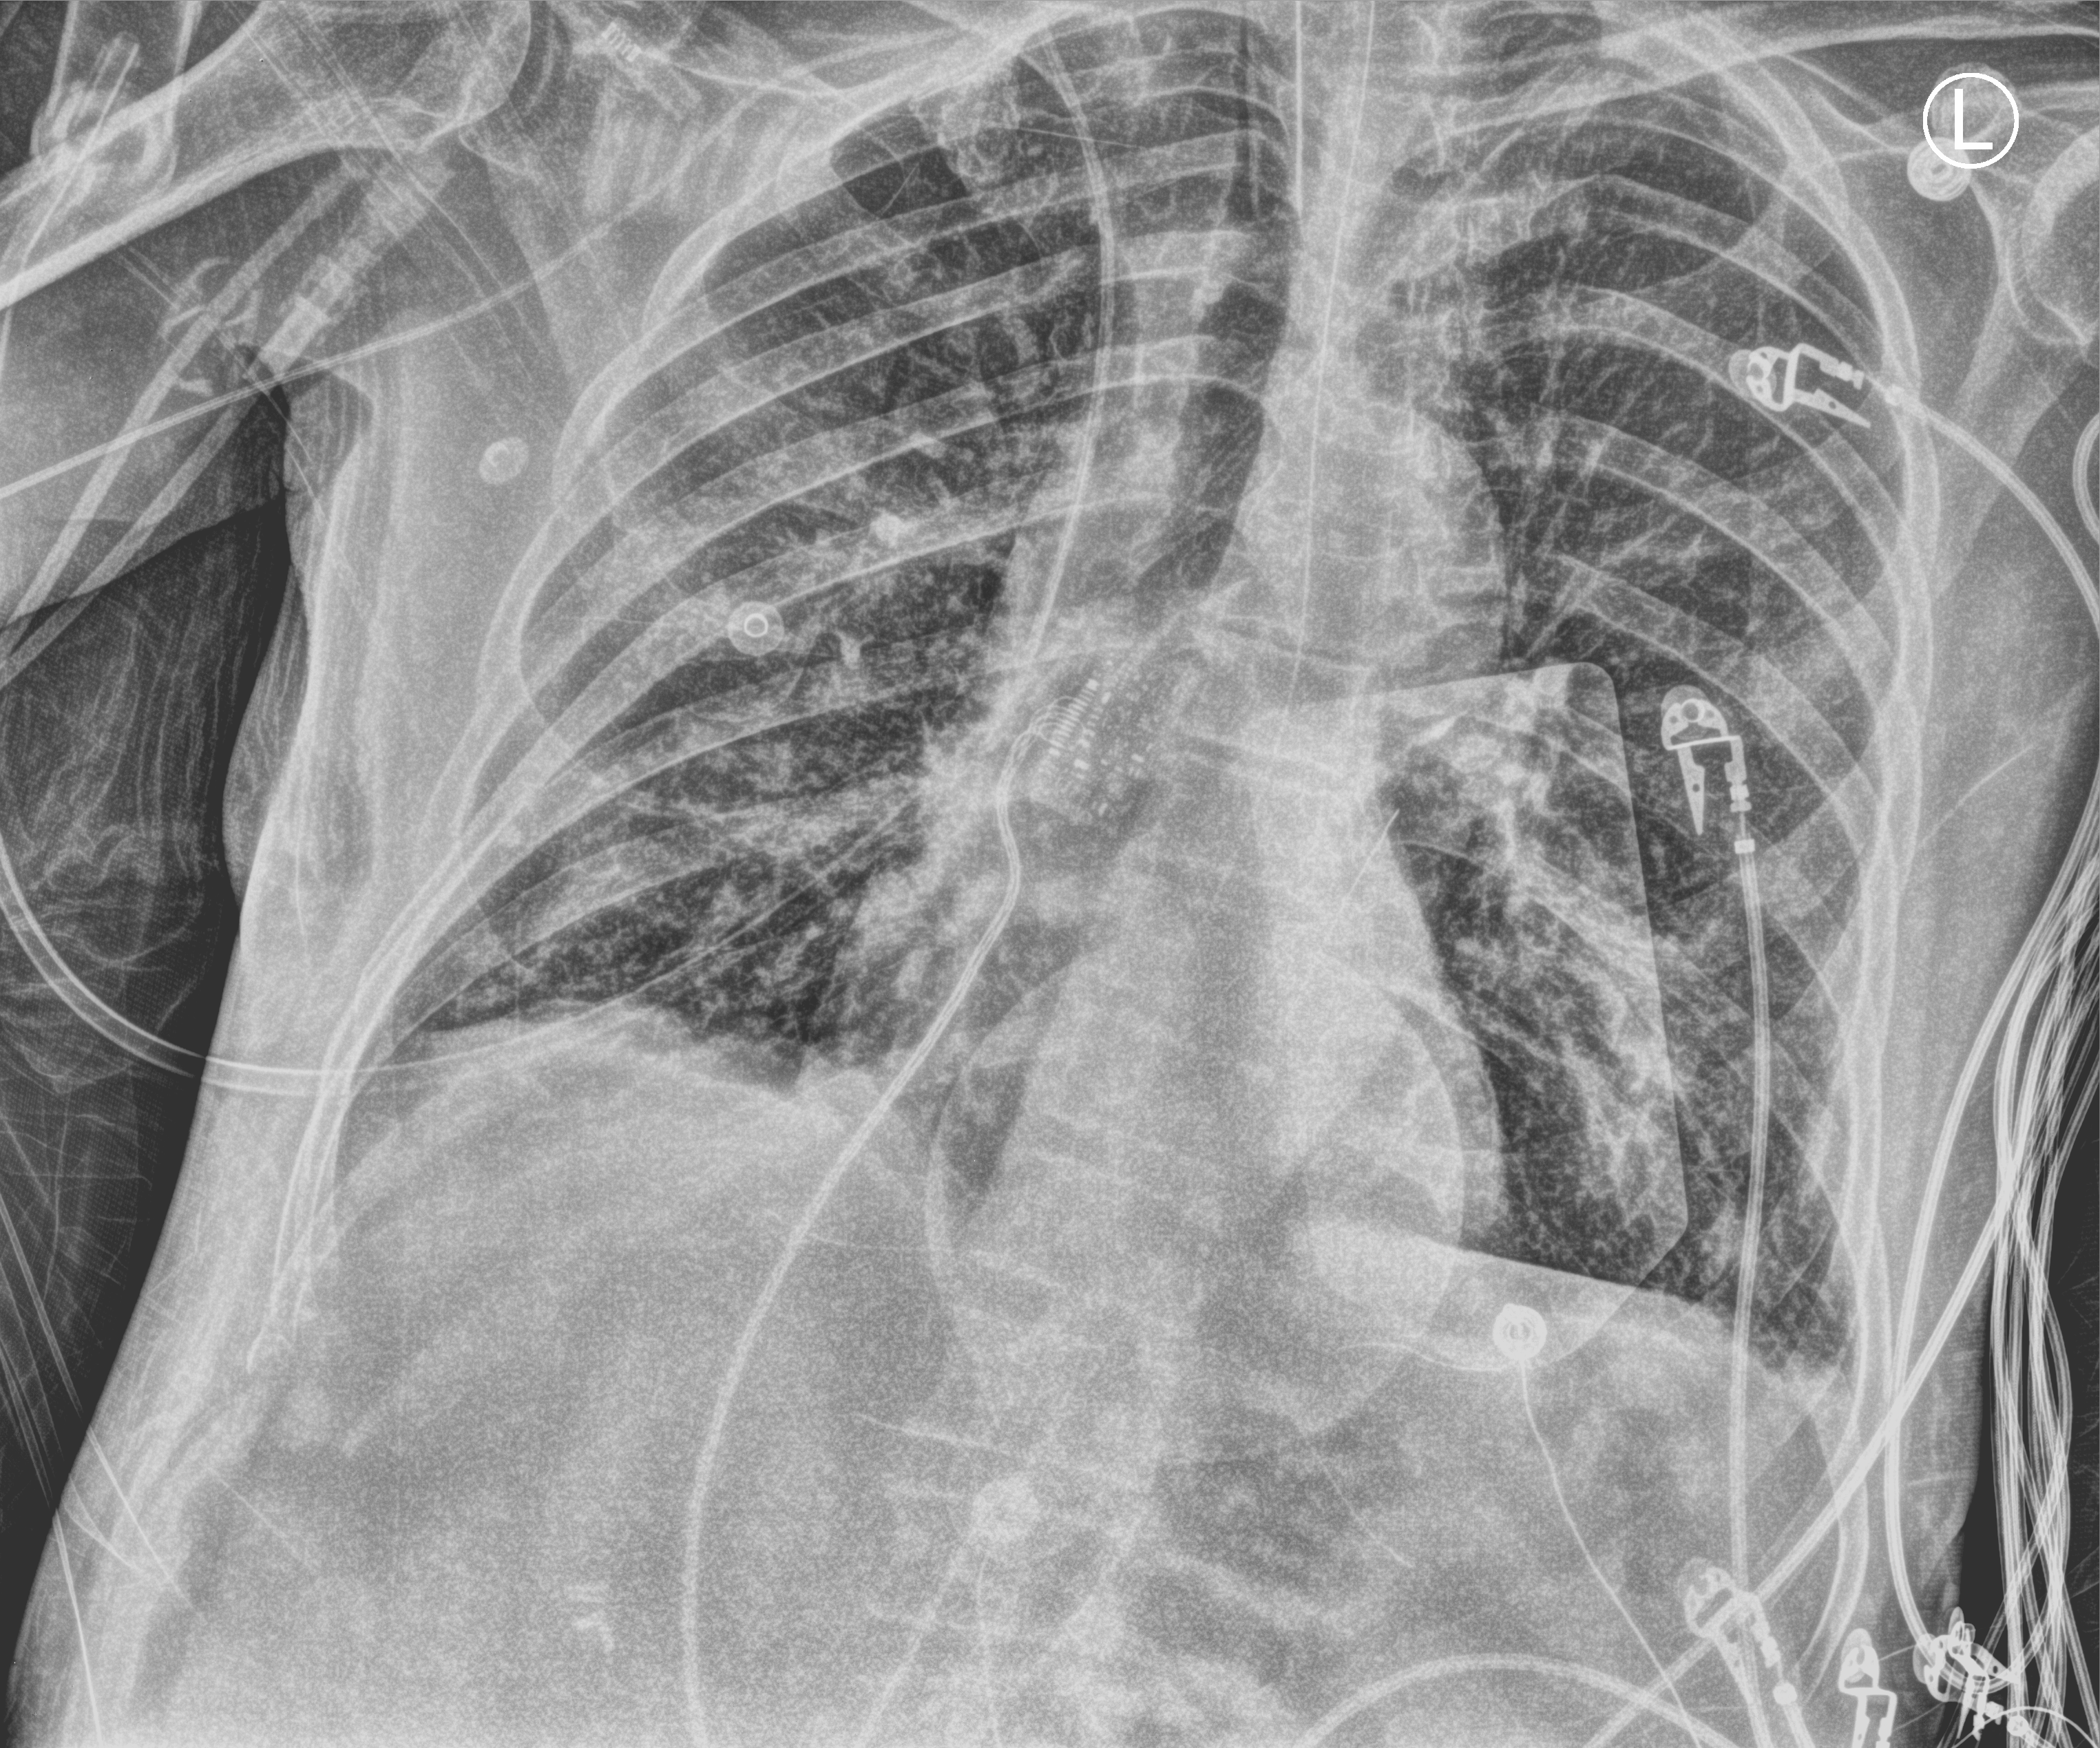
Chest X-ray (portable); anteroposterior (AP) projection. Male patient hospitalised with COVID-19, age 75–90 years.
Admission-level facts for this patient (not findings on this image; timing relative to this image not recorded): chronic kidney disease (admission record): no.